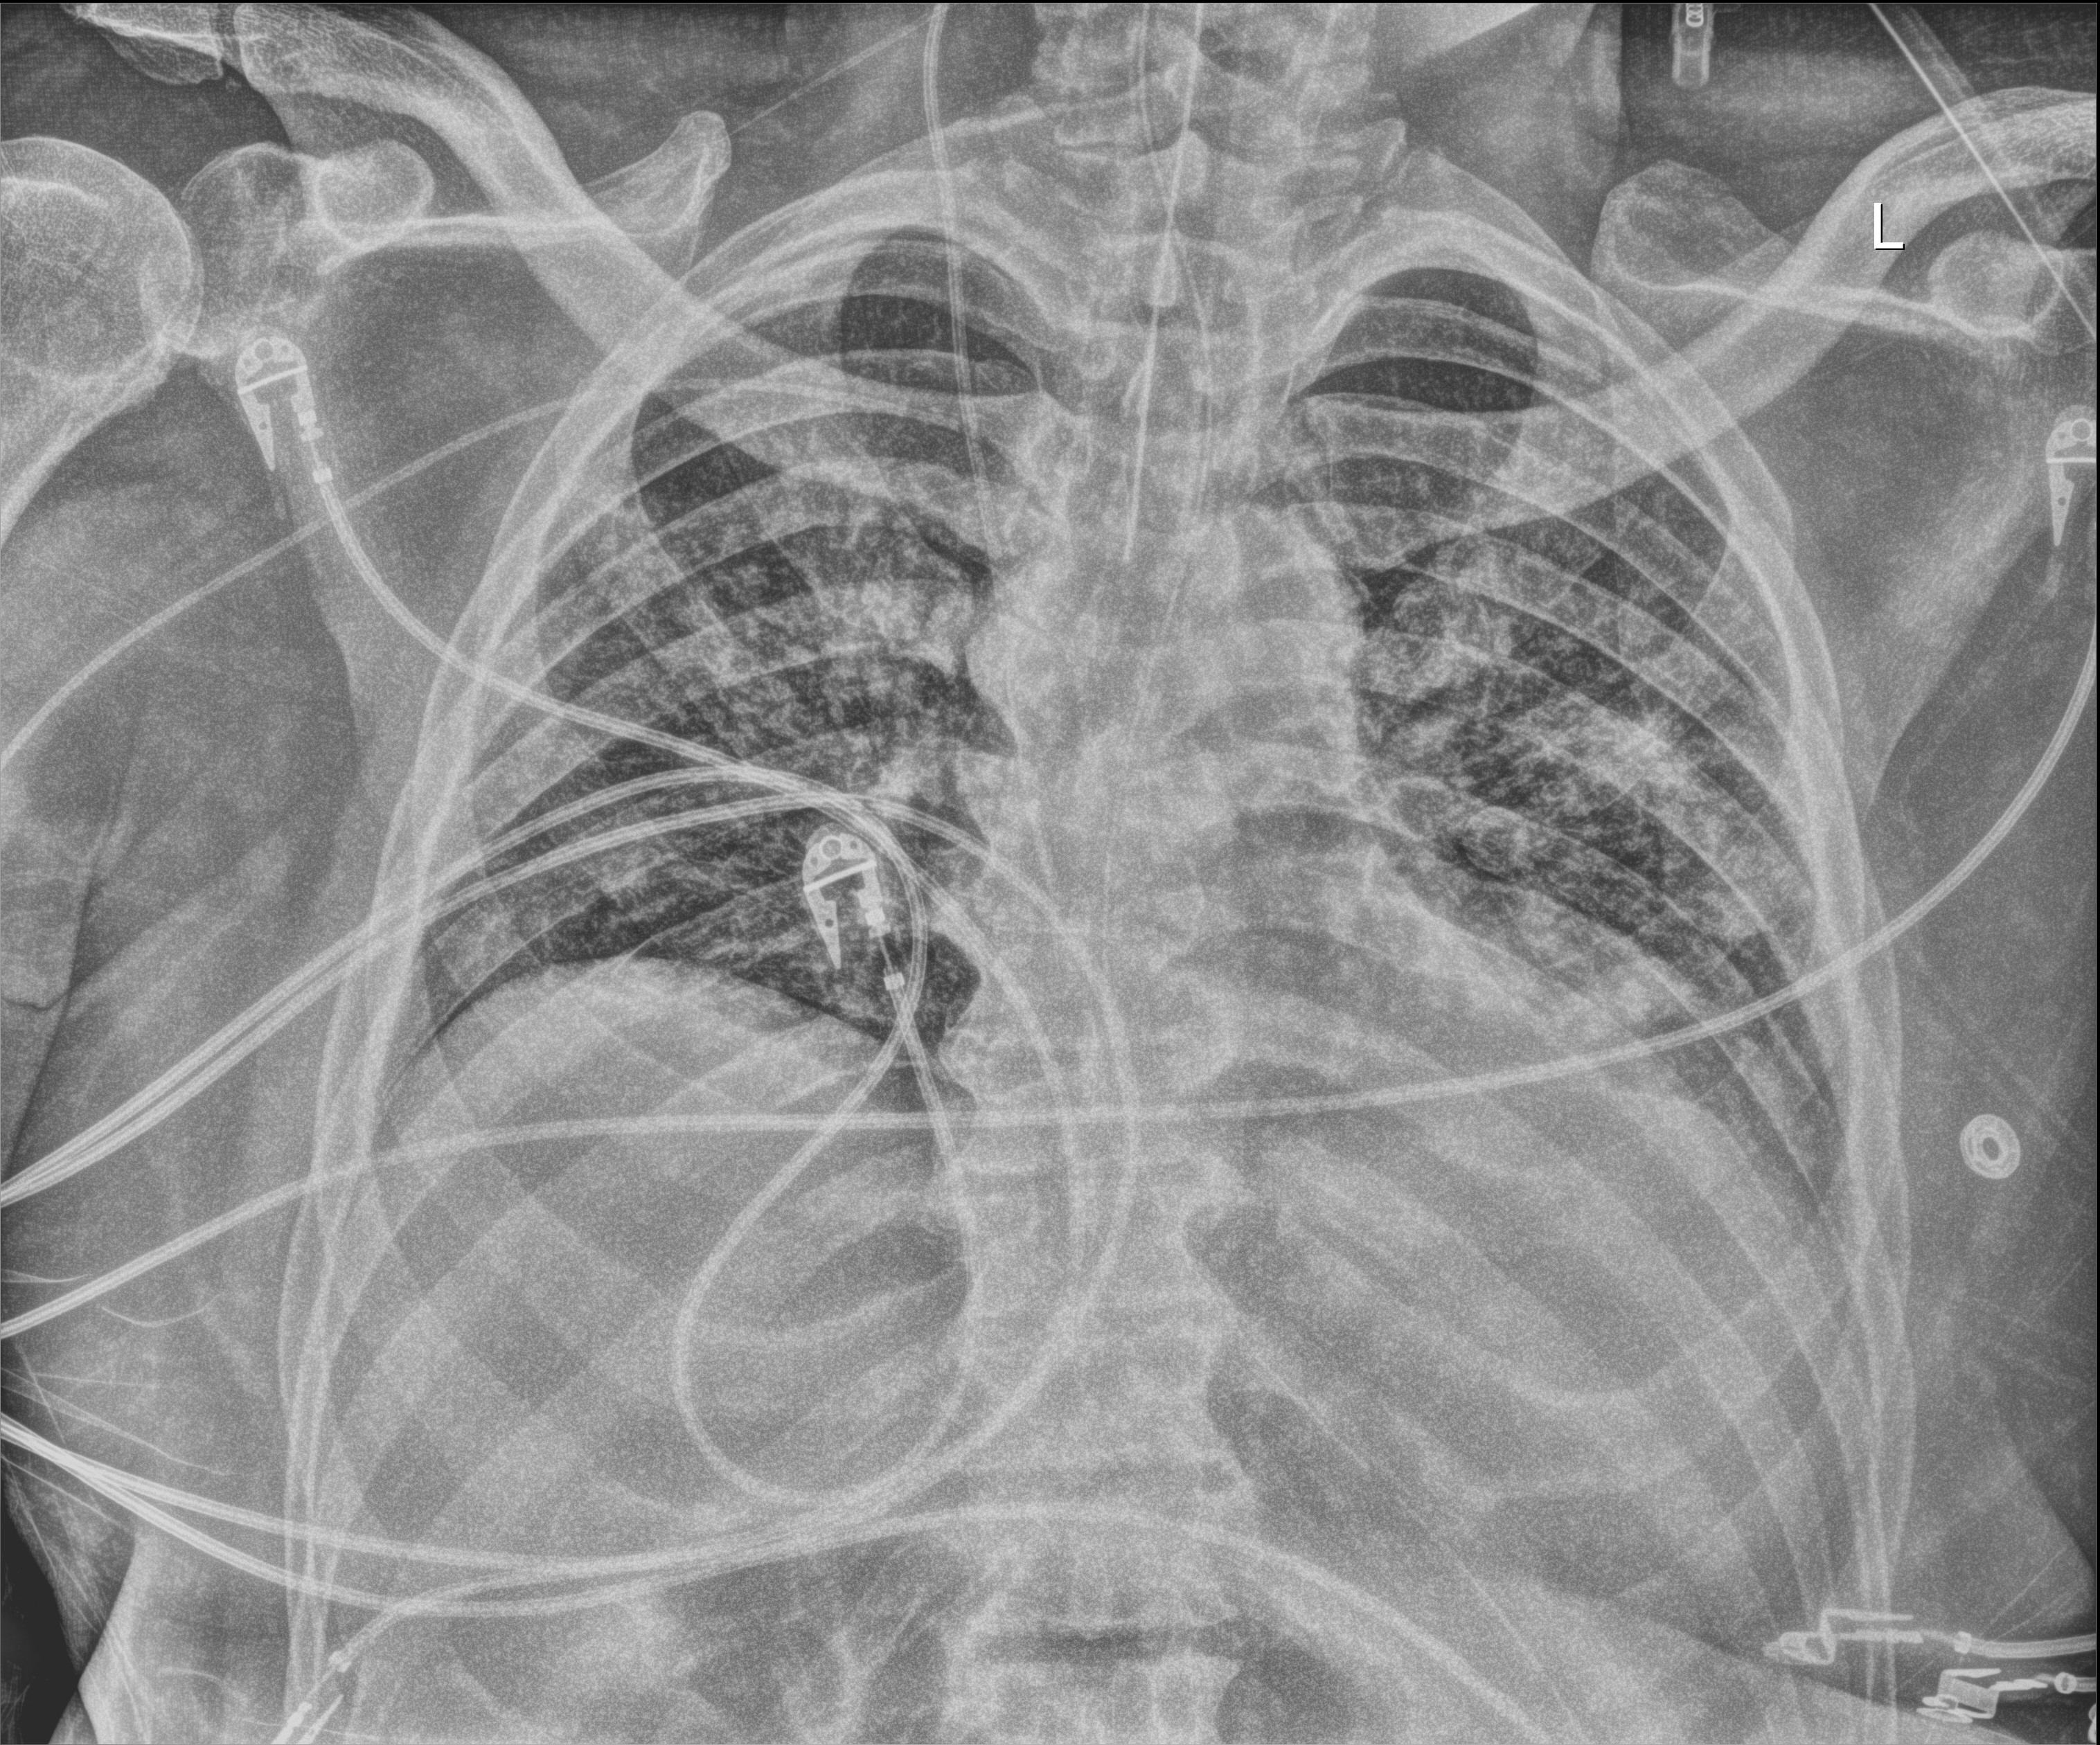
Bedside chest radiograph (digital radiography), anteroposterior (AP) projection. Patient hospitalised with COVID-19; male, aged 18–59 years.
Admission-level facts for this patient (not findings on this image; timing relative to this image not recorded):
- admitted to intensive care during this hospital stay: yes
- mechanically ventilated during this hospital stay: yes
- length of hospital stay: 41 days